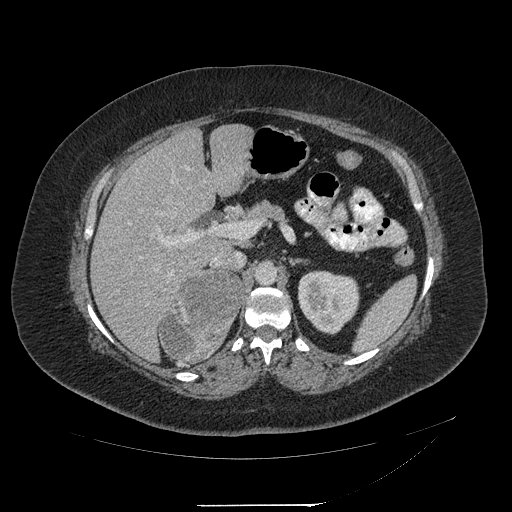
Contrast-enhanced abdominal CT, one axial slice; reconstruction kernel STANDARD; 120 kVp; intravenous contrast given; soft-tissue window (W 400 / L 40 HU); 1.25 mm slice thickness; 512 × 512 image matrix, field of view 453 × 453 mm. Female patient, age 55 years. Case-level facts recorded for this patient, not image findings: diagnosis: adrenocortical carcinoma; tumour side: right adrenal; tumour size at pathology: 11 cm; Ki-67 index: 20 %; stage (as recorded): 2.
Outlined on this slice (semi-automatic segmentation, software-assisted and operator-edited):
- mass: bounding box <162,273,243,361> (left, top, right, bottom; pixels)